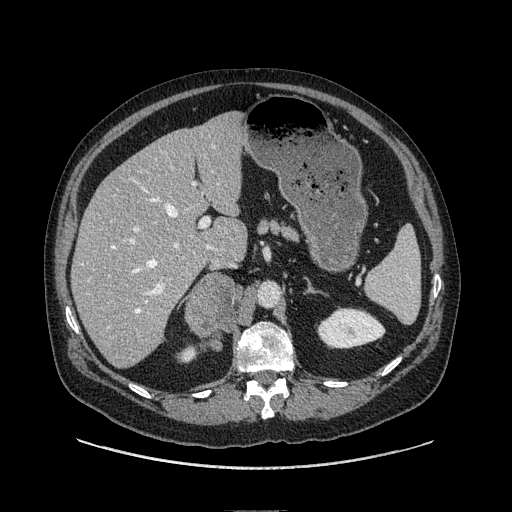
Contrast-enhanced abdominal CT, one axial slice; slice 56 of 149 in the series (ordered by position); soft-tissue window (W 400 / L 40 HU); 1.25 mm slice thickness; 512 × 512 image matrix, field of view 440 × 440 mm. Male patient. Case-level facts recorded for this patient, not image findings: diagnosis: adrenocortical carcinoma; tumour side: right adrenal; tumour size at pathology: 7.5 cm; Ki-67 index: 15 %; stage (as recorded): 2.
Structures marked on this image (semi-automatic segmentation, software-assisted and operator-edited):
- mass: bounding box [x1, y1, x2, y2] px = [187, 274, 240, 339]